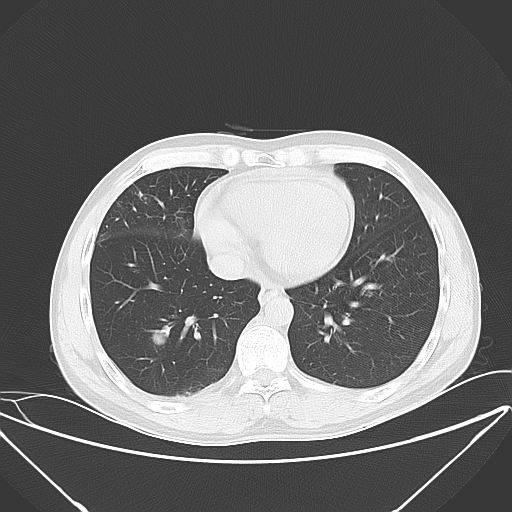
Chest CT, one axial slice; slice 19 of 56 in the series (ordered by position); 120 kVp; lung window (W 1500 / L -600 HU); 5 mm slice thickness; 512 × 512 image matrix, field of view 397 × 397 mm. Male patient, age 42 years. Case-level facts recorded for this patient, not image findings: clinical TNM (as recorded): T1b N3 M1b.
Outlined on this slice (bounding box drawn by a radiologist):
- lung tumour (recorded histology: small cell carcinoma): box from (x=149, y=324) to (x=174, y=350) px